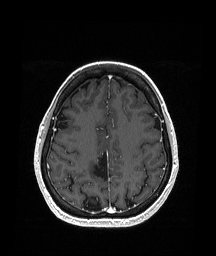
Brain MRI from a brain-tumour surgery series, one axial slice. T1-weighted post-contrast. 1.05 mm slice thickness. 216 × 256 image matrix. Case-level facts recorded for this patient, not image findings: histopathology: Oligodendroglioma; WHO grade: 2; IDH mutation: yes; tumour location: Right Parietal.
Annotated regions visible in this slice (outlined manually by an expert reader):
- previous resection cavity: bounding box <94,149,109,183> (left, top, right, bottom; pixels)